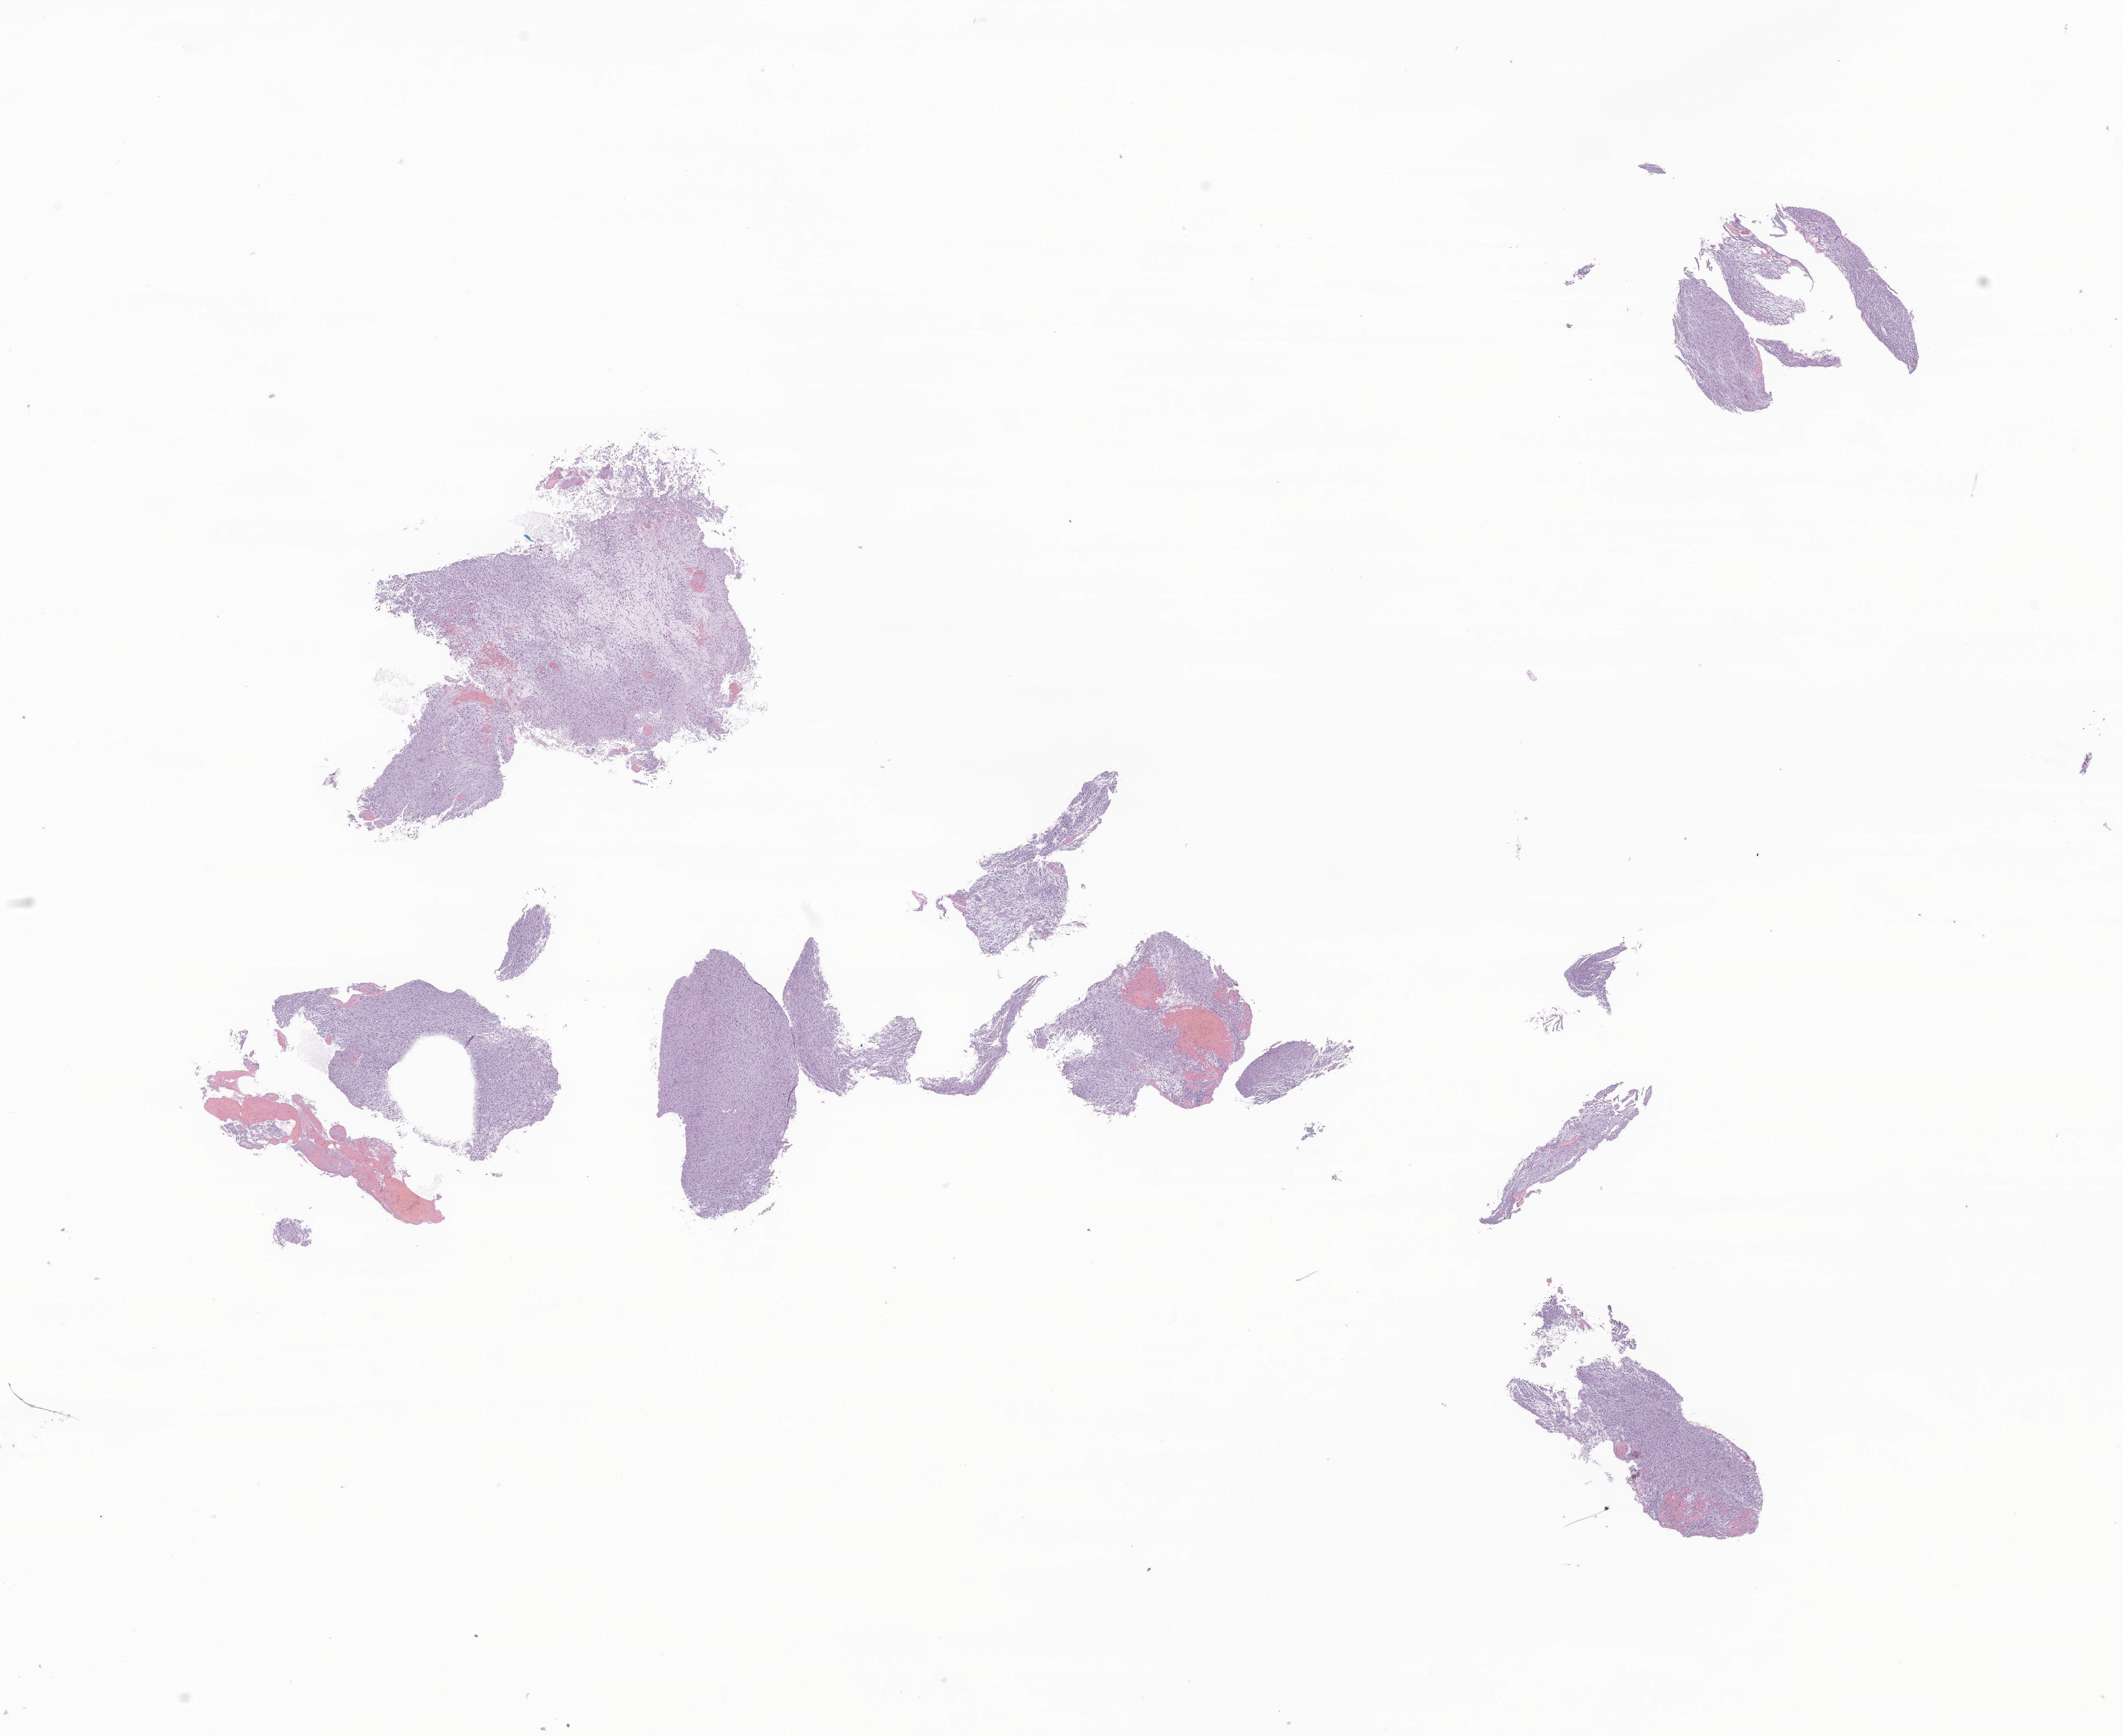
Digitized hematoxylin and eosin (H&E)-stained section of tumor tissue from the cerebral ventricle — whole scanned area (about 20.6 x 16.9 mm) shown as a low-resolution overview; formalin-fixed, paraffin-embedded (FFPE) tissue. Patient female; age 88 months (7 years 4 months).
Recorded diagnosis: Glioma, malignant.